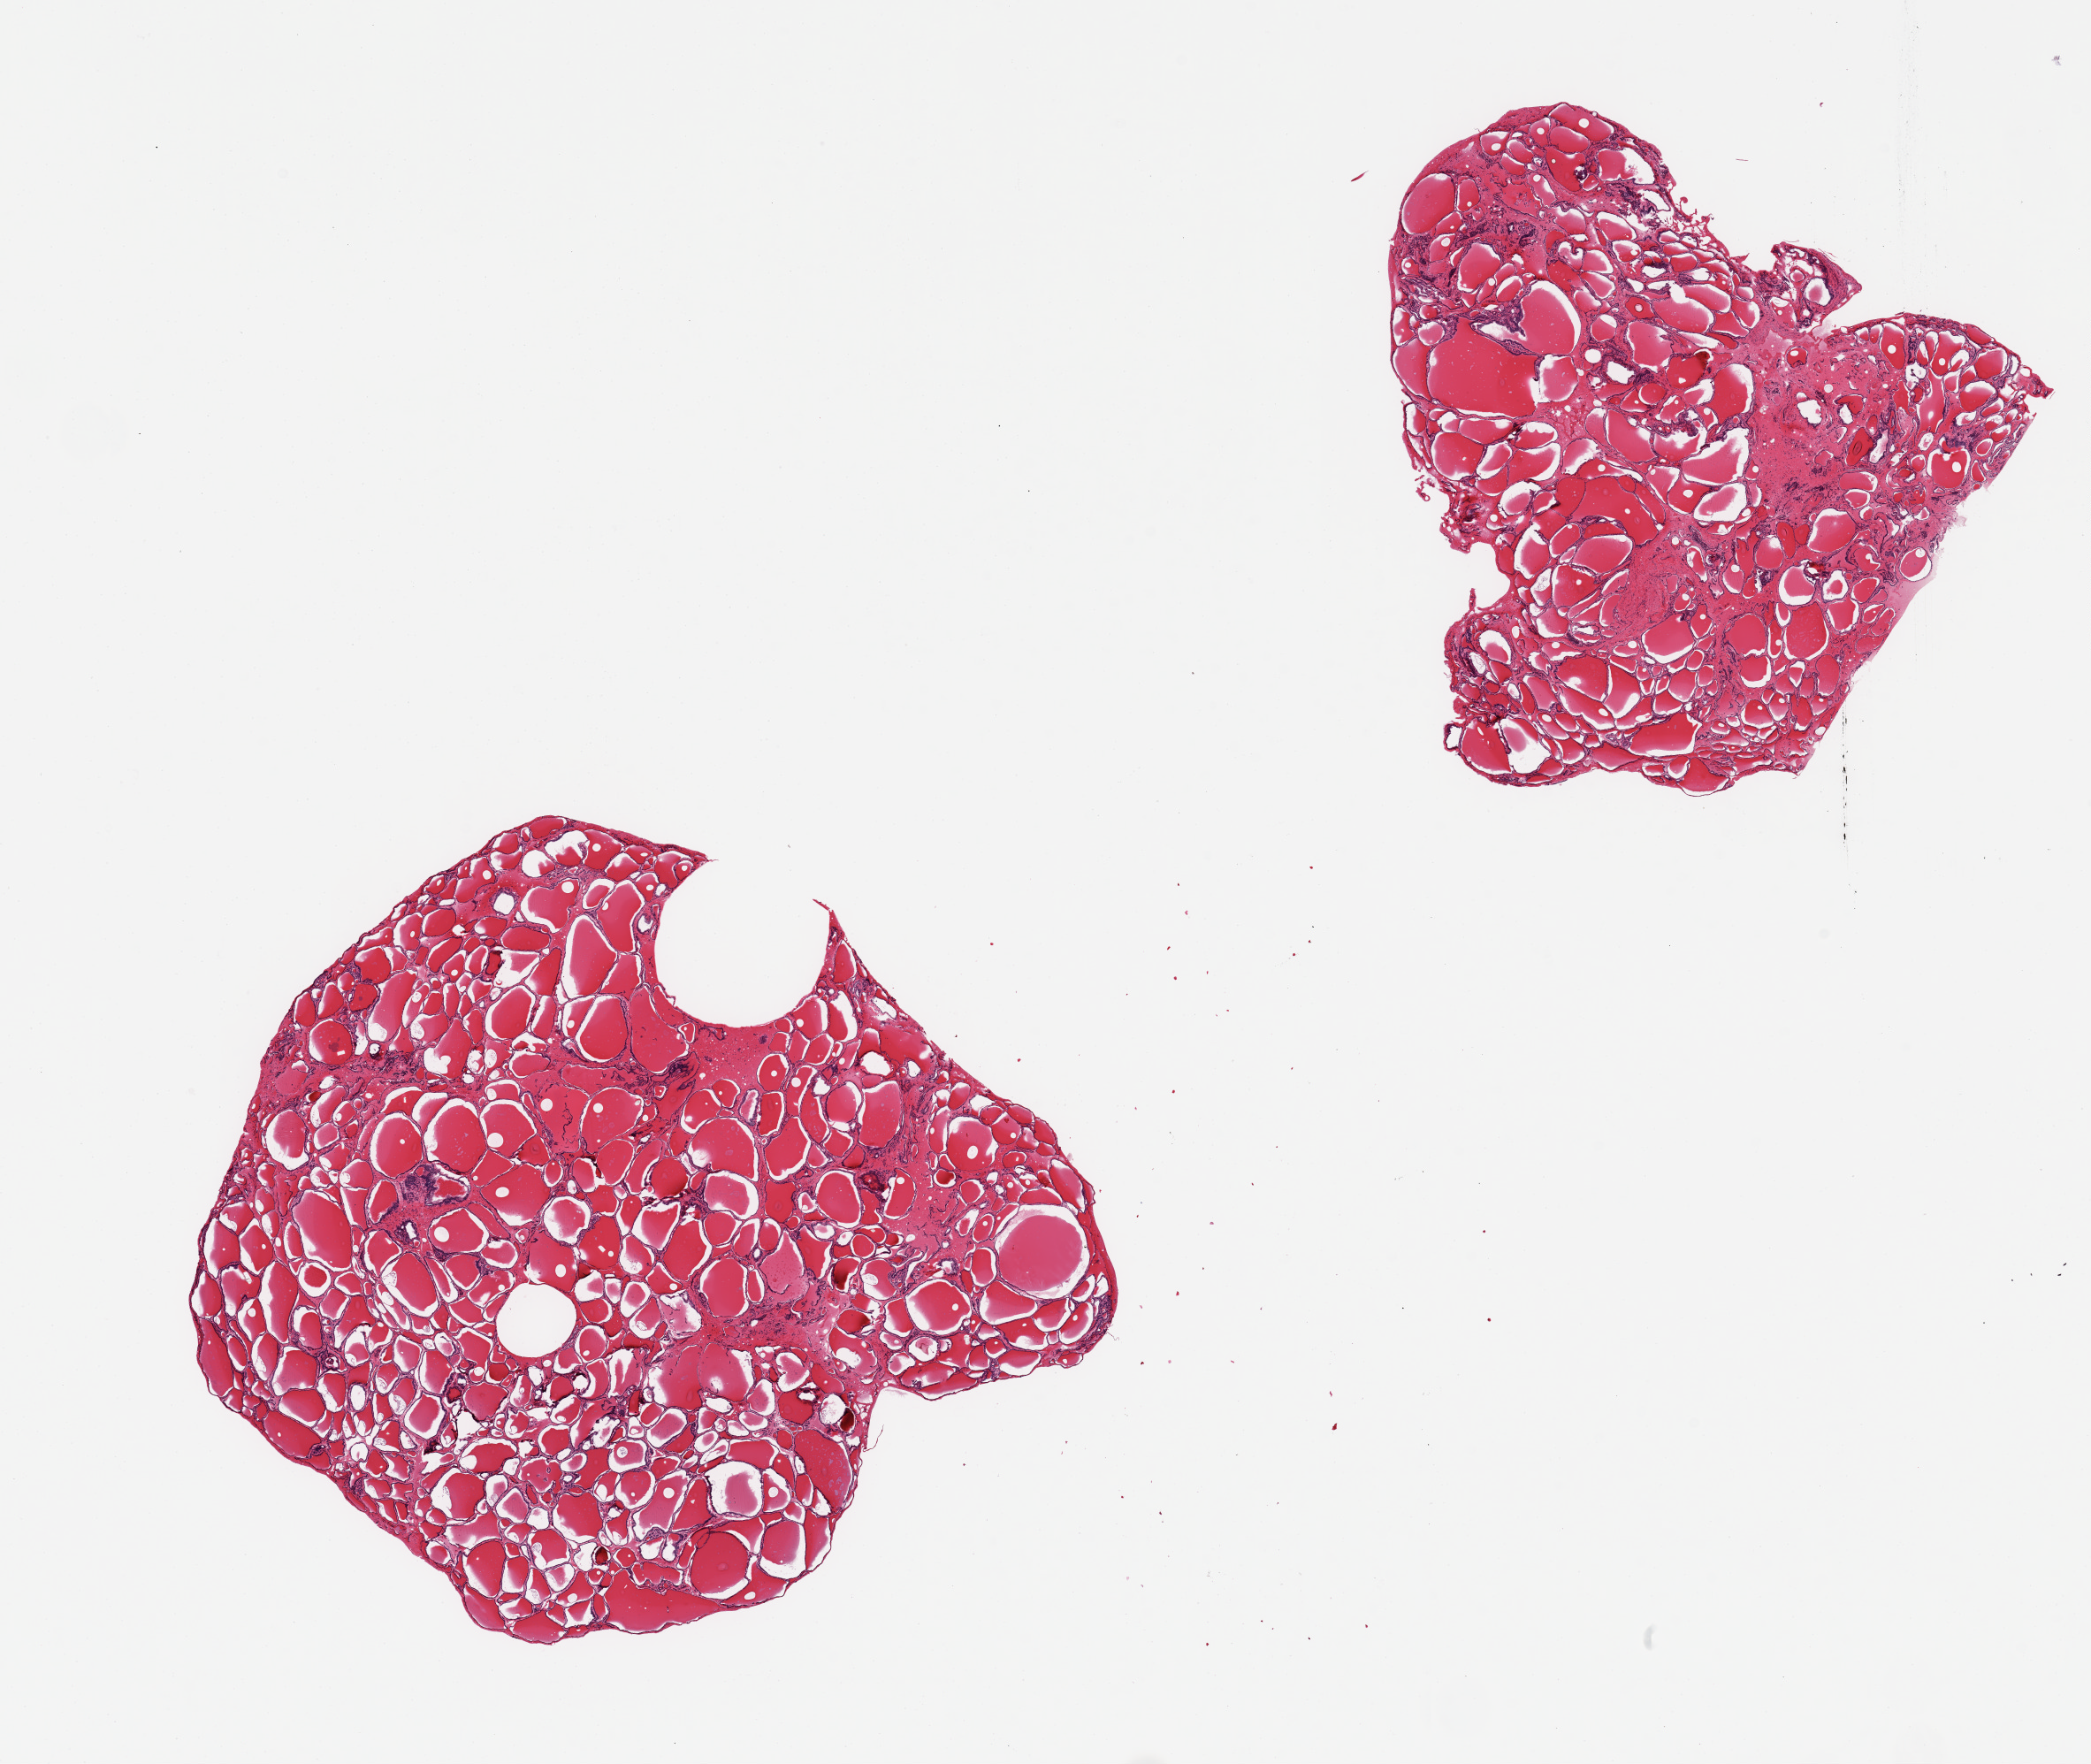
Digitized haematoxylin and eosin-stained section, brightfield — low-resolution overview of the scanned area, about 18.7 x 15.8 mm (acquisition: 20x scan). PAXgene-fixed paraffin-embedded (PFPE) section. Section of thyroid (target tissue). Donor tissue sample. Male donor.
Pathologist's review note for this sample: 2 pieces; focal fibrosis/scarring.